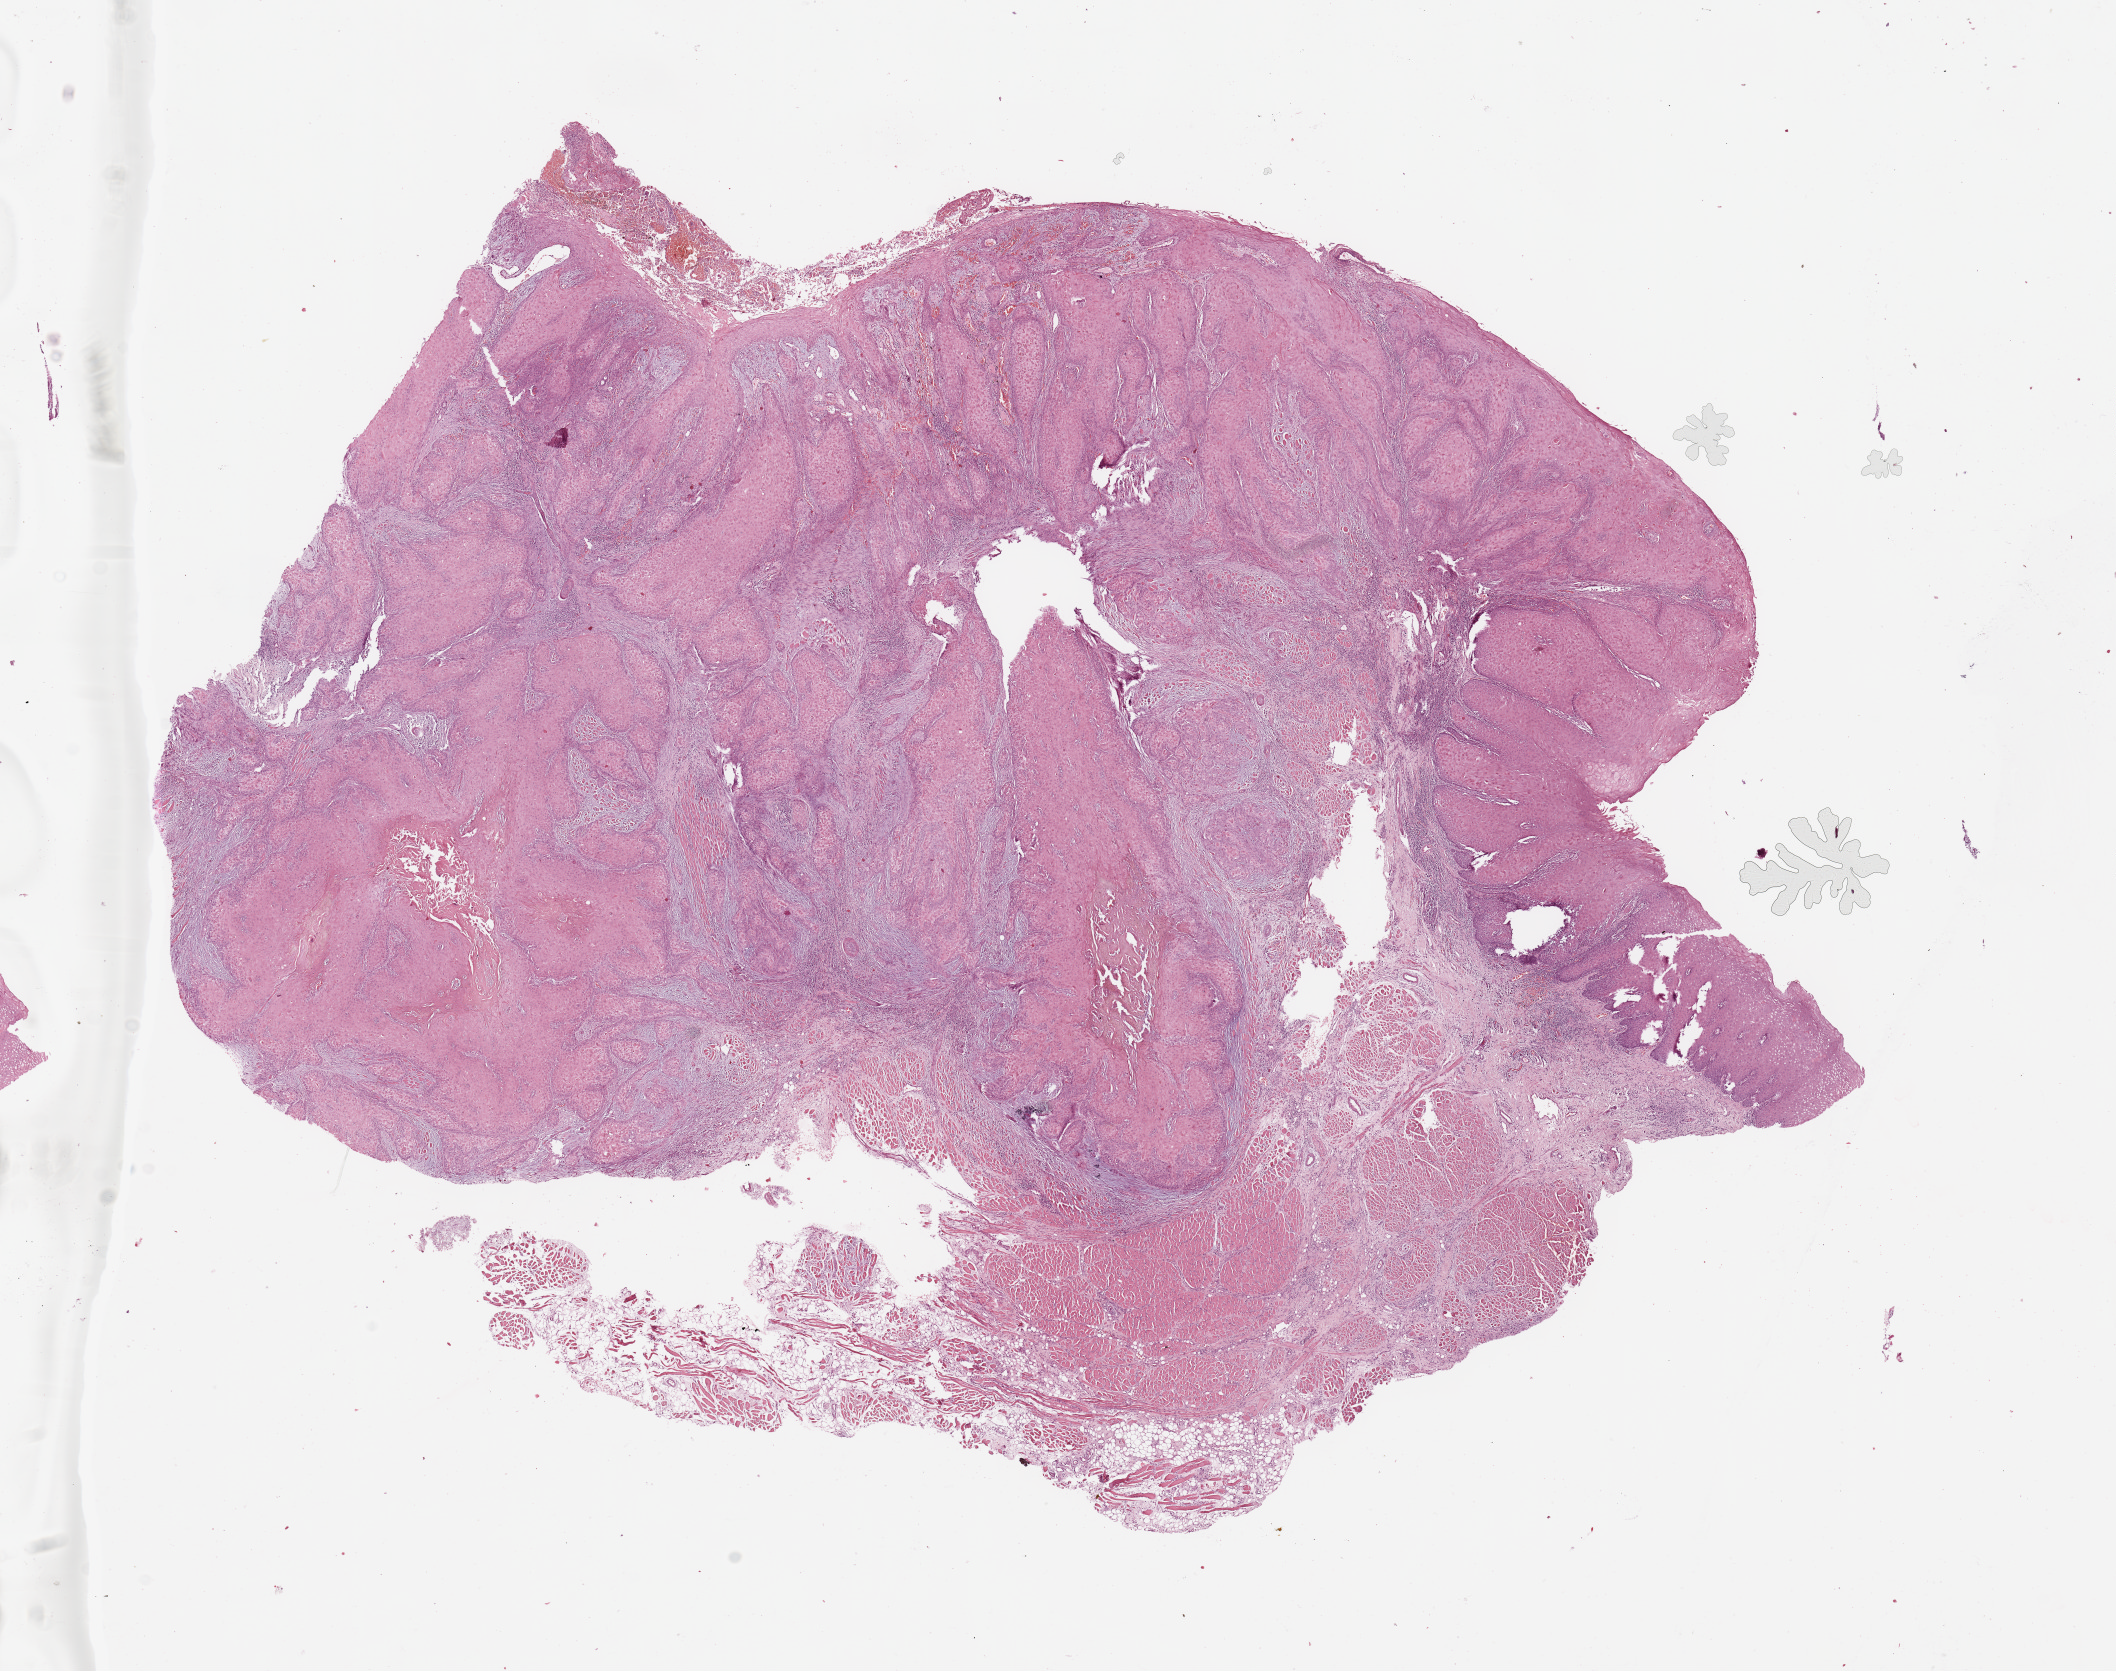
Hematoxylin and eosin (H&E) stained whole-slide image, low-resolution overview of the scanned area, about 16.7 x 13.2 mm (from a 20x scan); head and neck, tissue type not recorded. Patient: male, age 54 years.
Patient diagnosis: Squamous cell carcinoma, NOS (tongue, NOS).